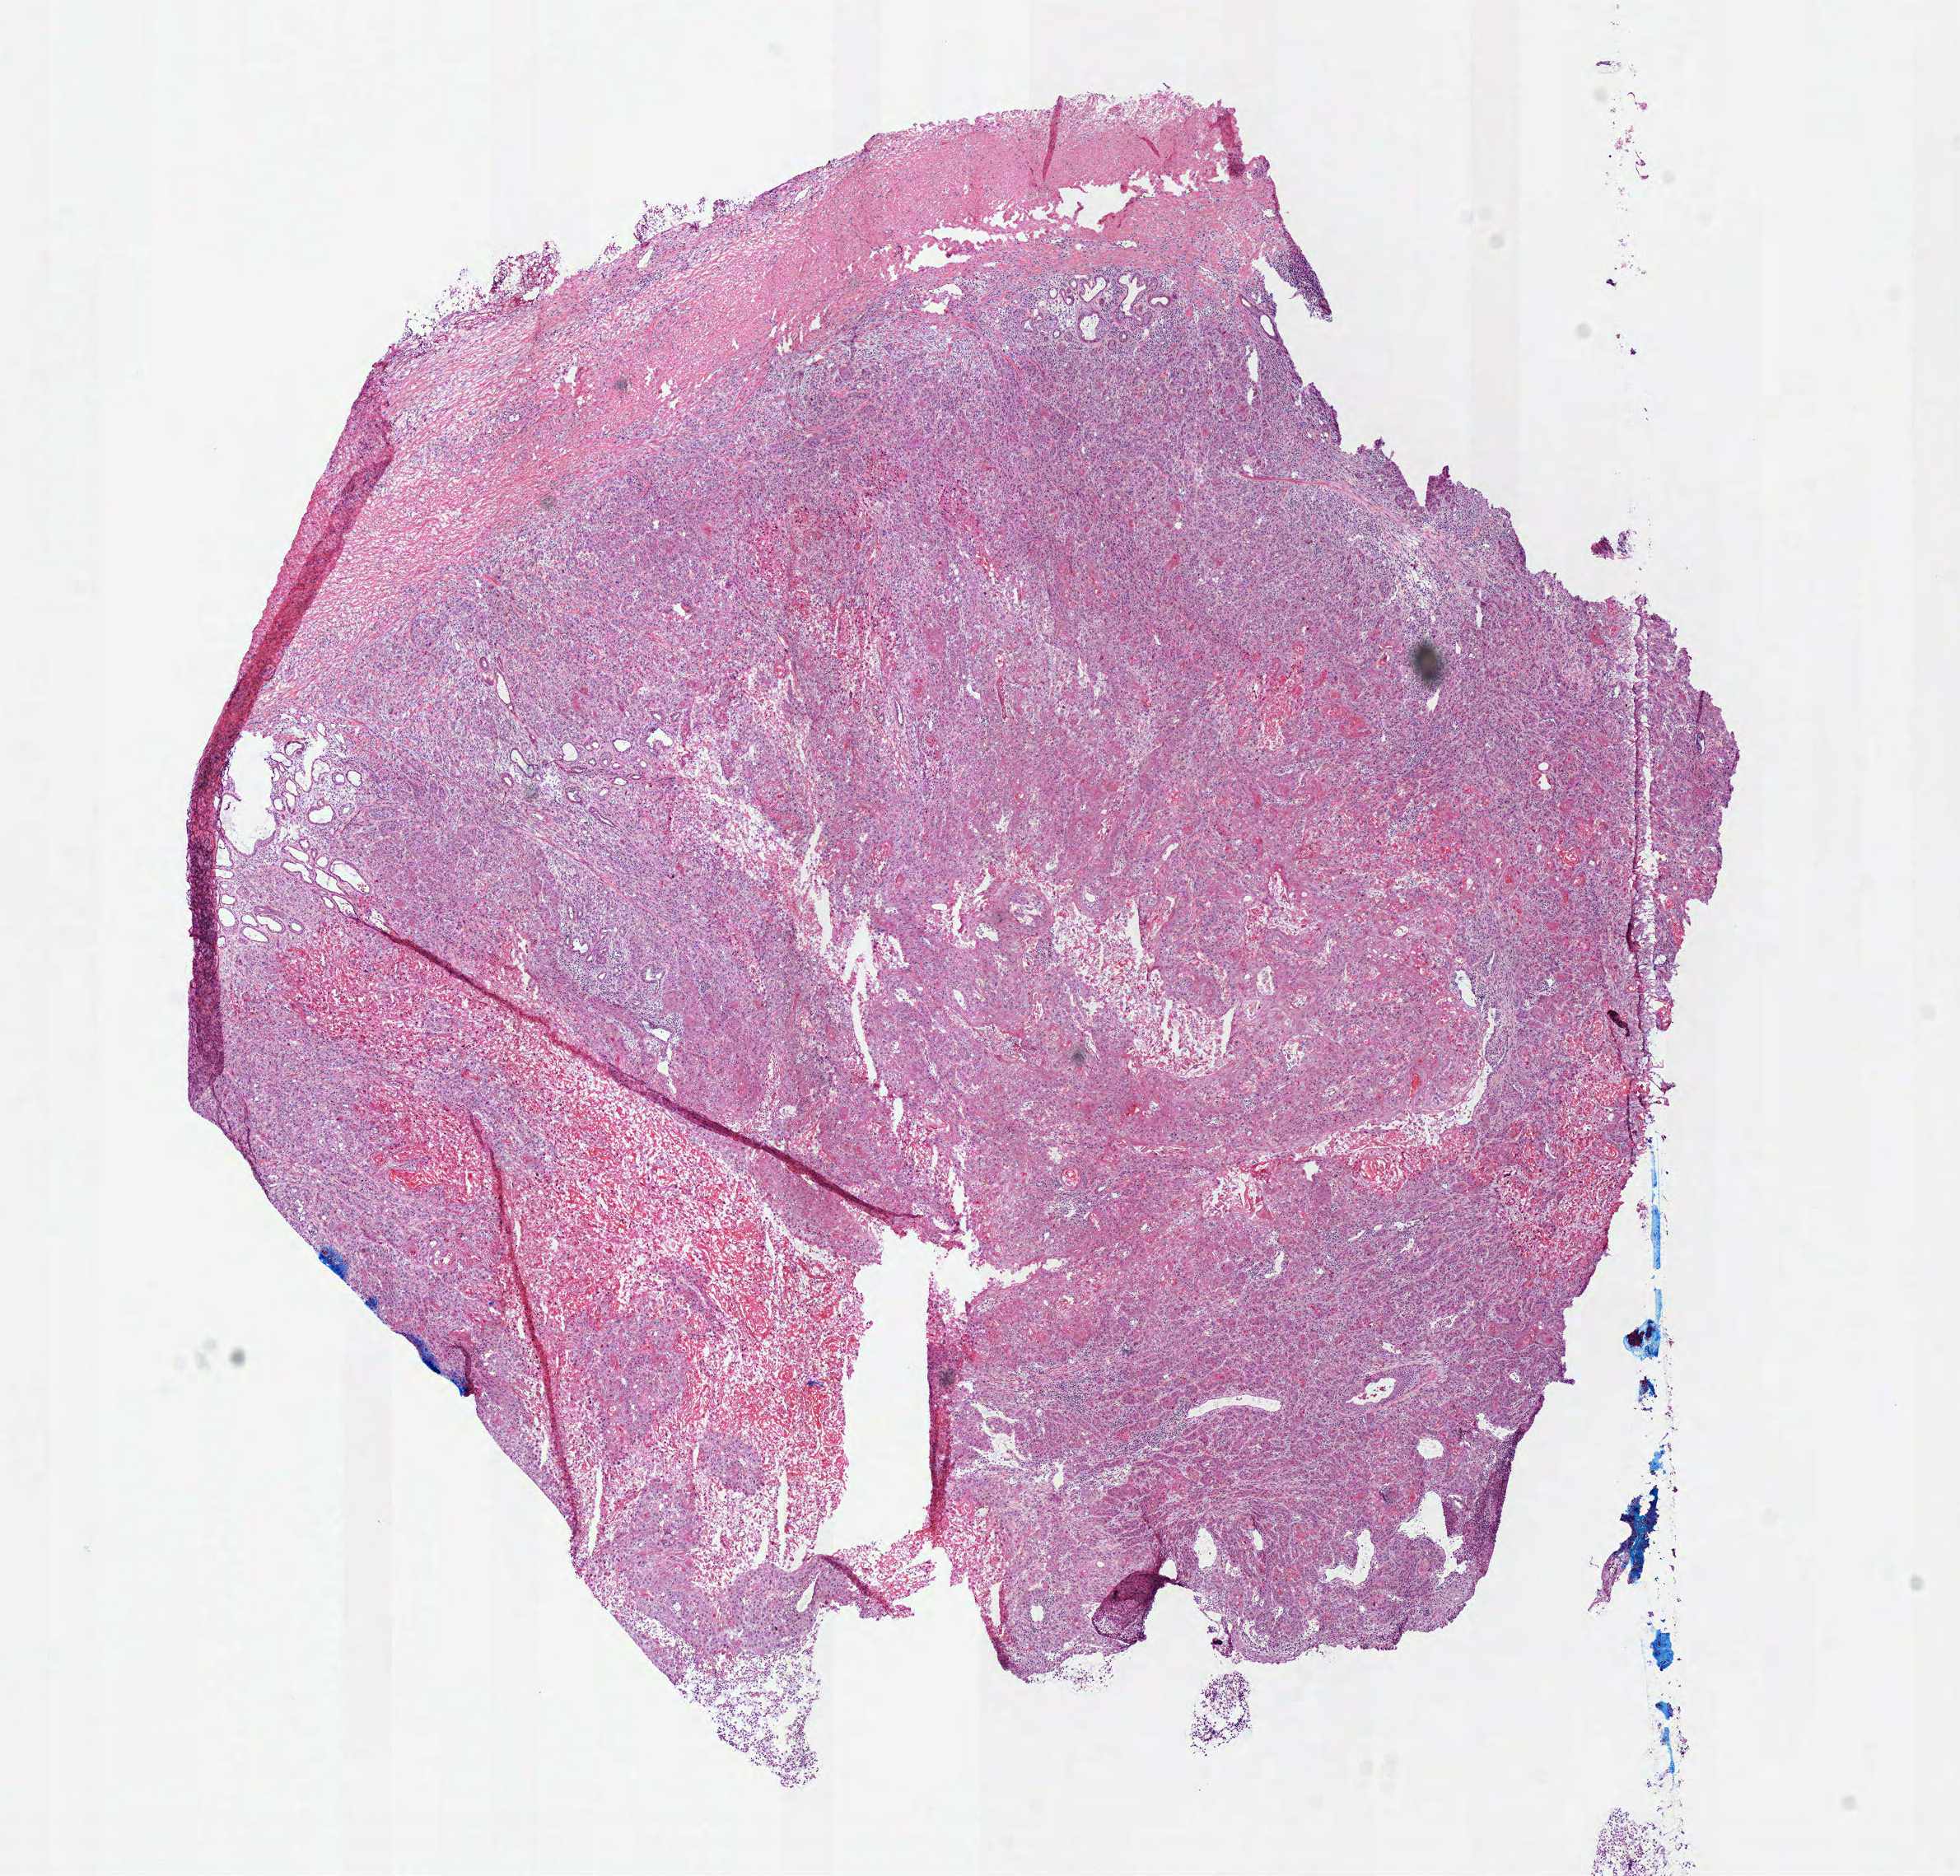
H&E whole-slide image — a low-resolution overview of the entire scanned area, about 9.4 x 9.0 mm (slide scanned at 40x). Frozen section from the bottom of the tissue portion. Head and neck, primary tumour sample. Female patient; age at initial diagnosis 64 years. Histologic grade: G2 (moderately differentiated). Composition of this section per pathologist review: tumour cells 92%, tumour nuclei 85%, normal cells 0%, stromal cells 5%, necrosis 3%.
AJCC pathologic stage: IVA (7th edition). Laterality: midline. Pathologic diagnosis: Squamous cell carcinoma, NOS (larynx, NOS).